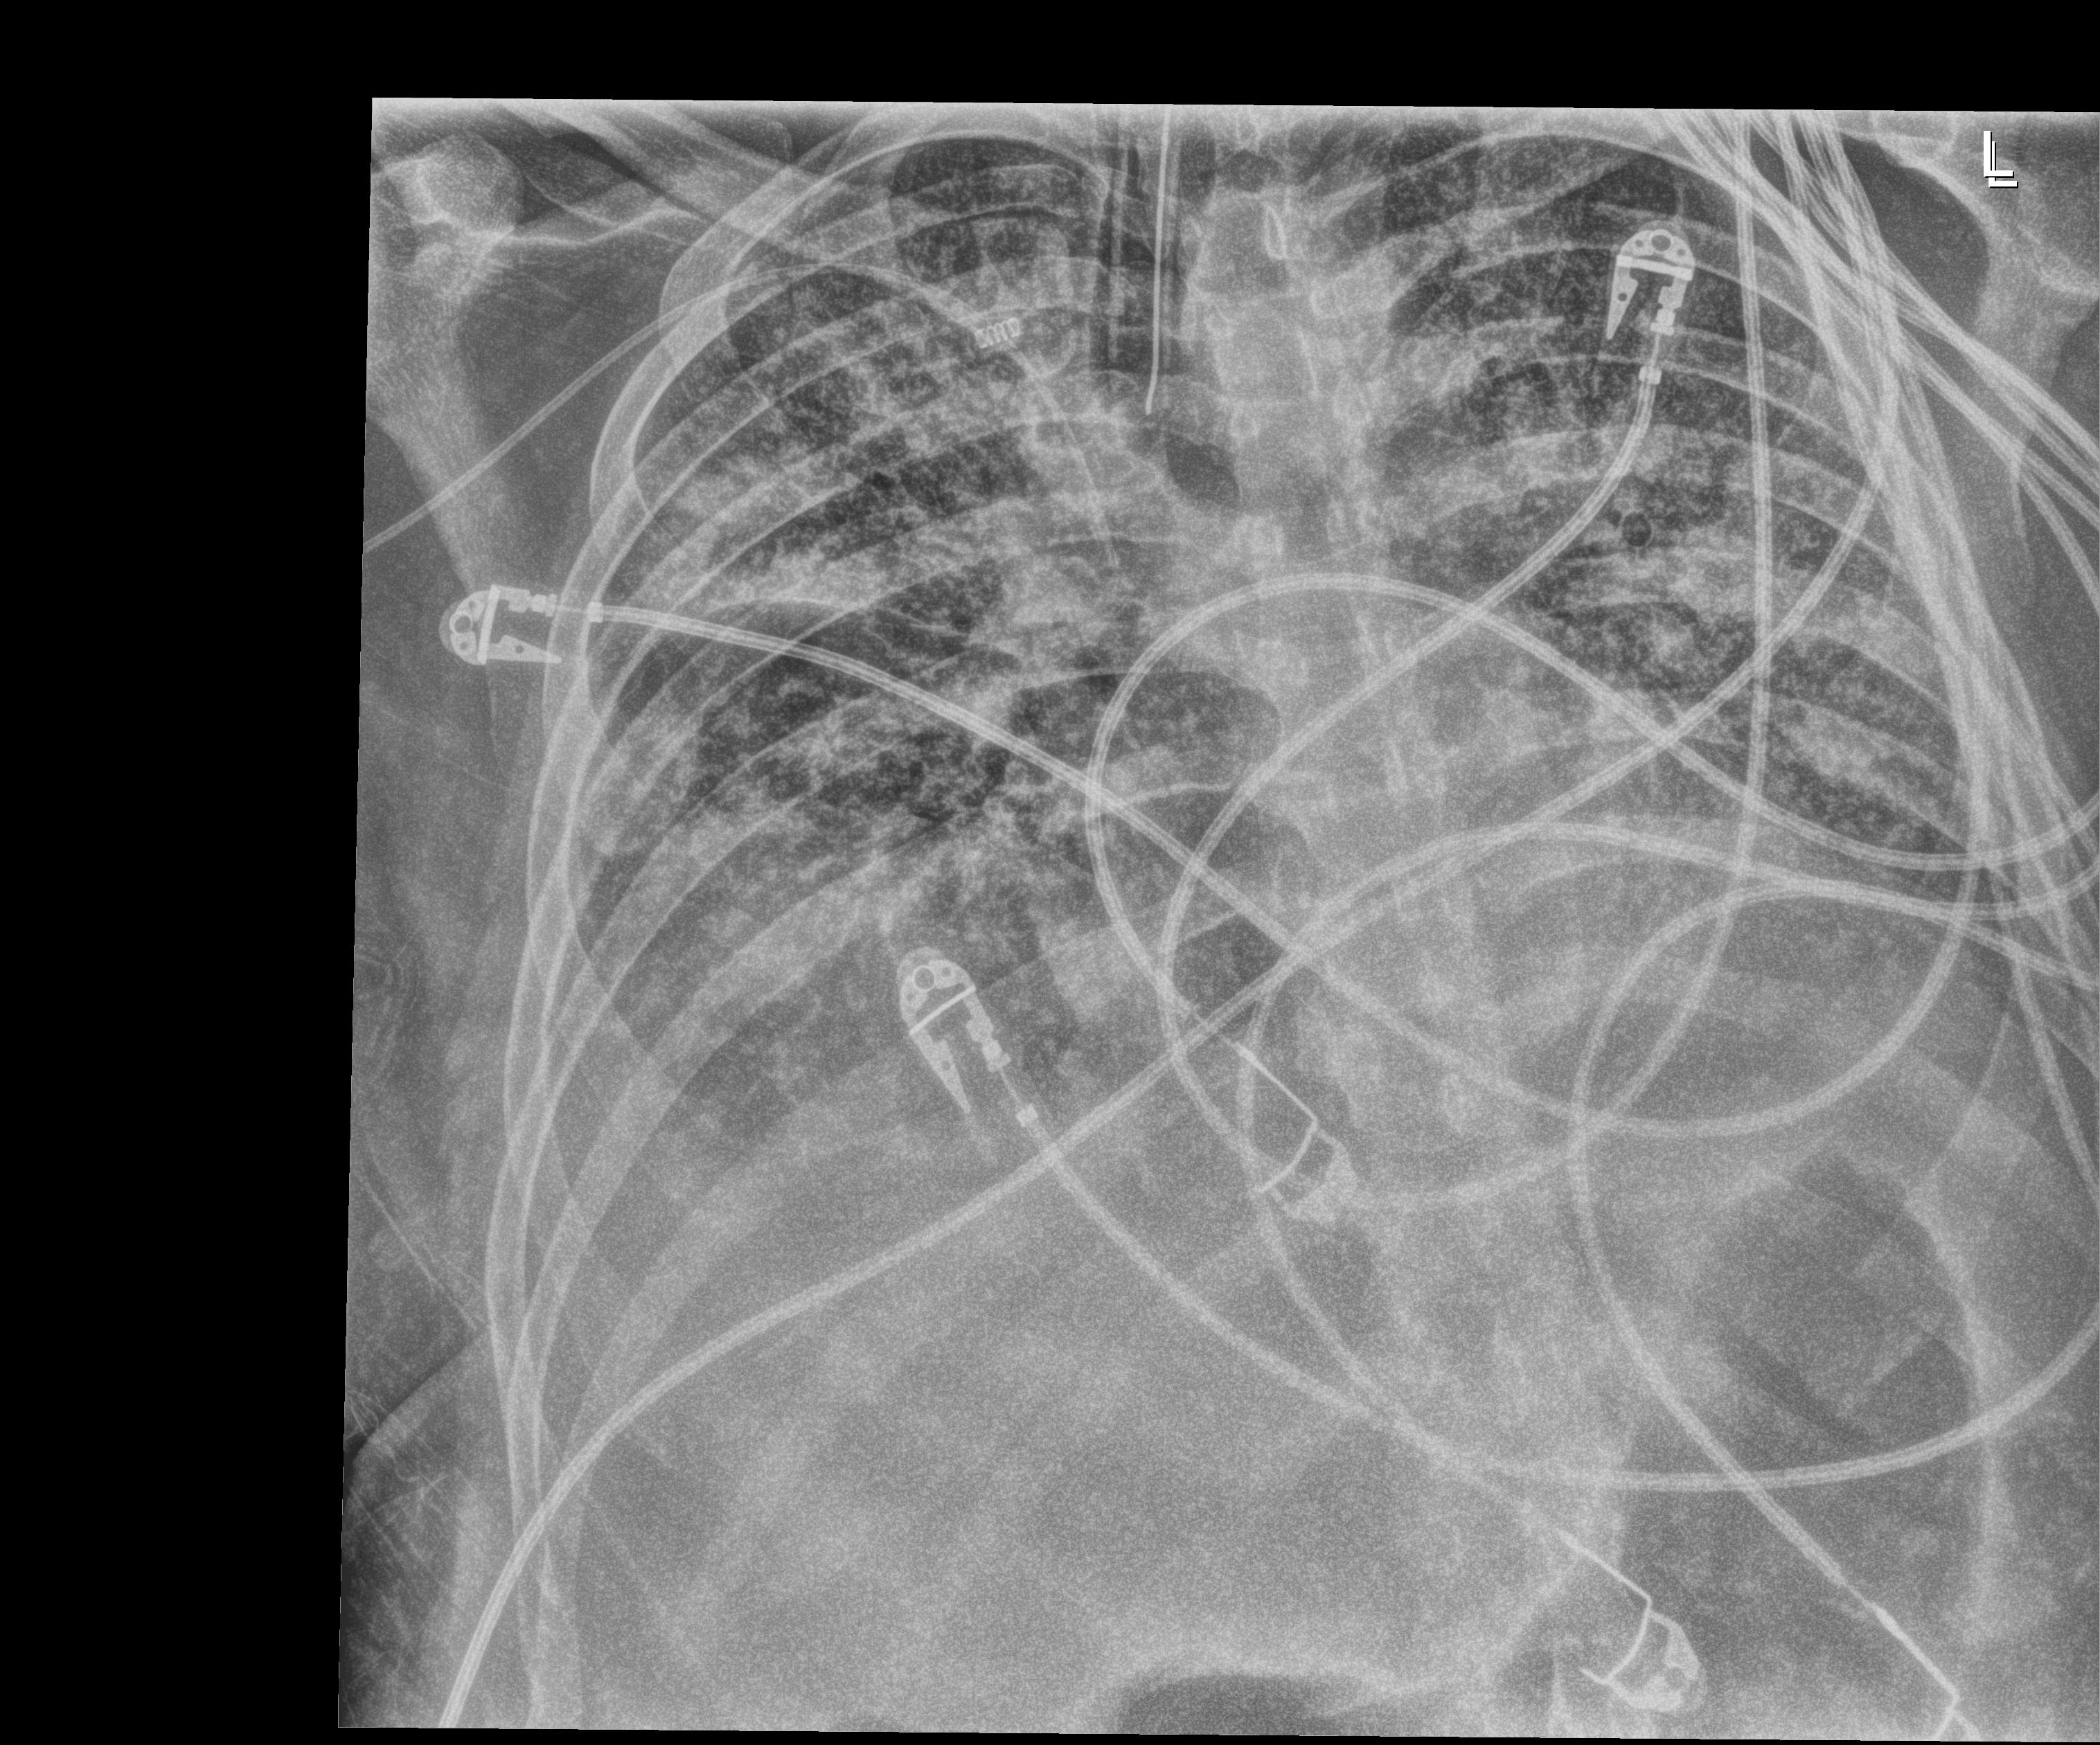
Chest X-ray (portable), anteroposterior (AP) projection. Male patient hospitalised with COVID-19, age 18–59 years.
From the hospital-stay record, not from the radiograph (when in the stay this image was taken is not recorded): admitted to intensive care during this hospital stay: yes; other chronic lung disease (admission record): no.